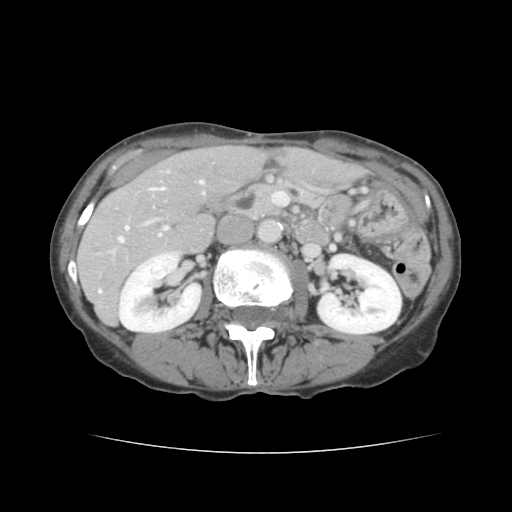
Contrast-enhanced abdominal CT, one axial slice; slice 62 of 136 in the series (ordered by position); intravenous contrast given; soft-tissue window (W 400 / L 40 HU); 512 × 512 image matrix, field of view 319 × 319 mm. Female patient, age 77 years. Case-level facts recorded for this patient, not image findings: diagnosis: colorectal cancer liver metastases, imaged before liver resection; multiple liver metastases: yes; largest metastasis: 3 cm.
Annotated regions visible in this slice (expert manual segmentation):
- hepatic veins: bounding box (x1, y1, x2, y2) in pixels: (119, 181, 204, 242)
- liver: (78, 146, 360, 323)
- planned liver remnant (the part of the liver to remain after resection): (163, 146, 361, 204)
- portal vein (with intrahepatic branches): (99, 226, 168, 292)